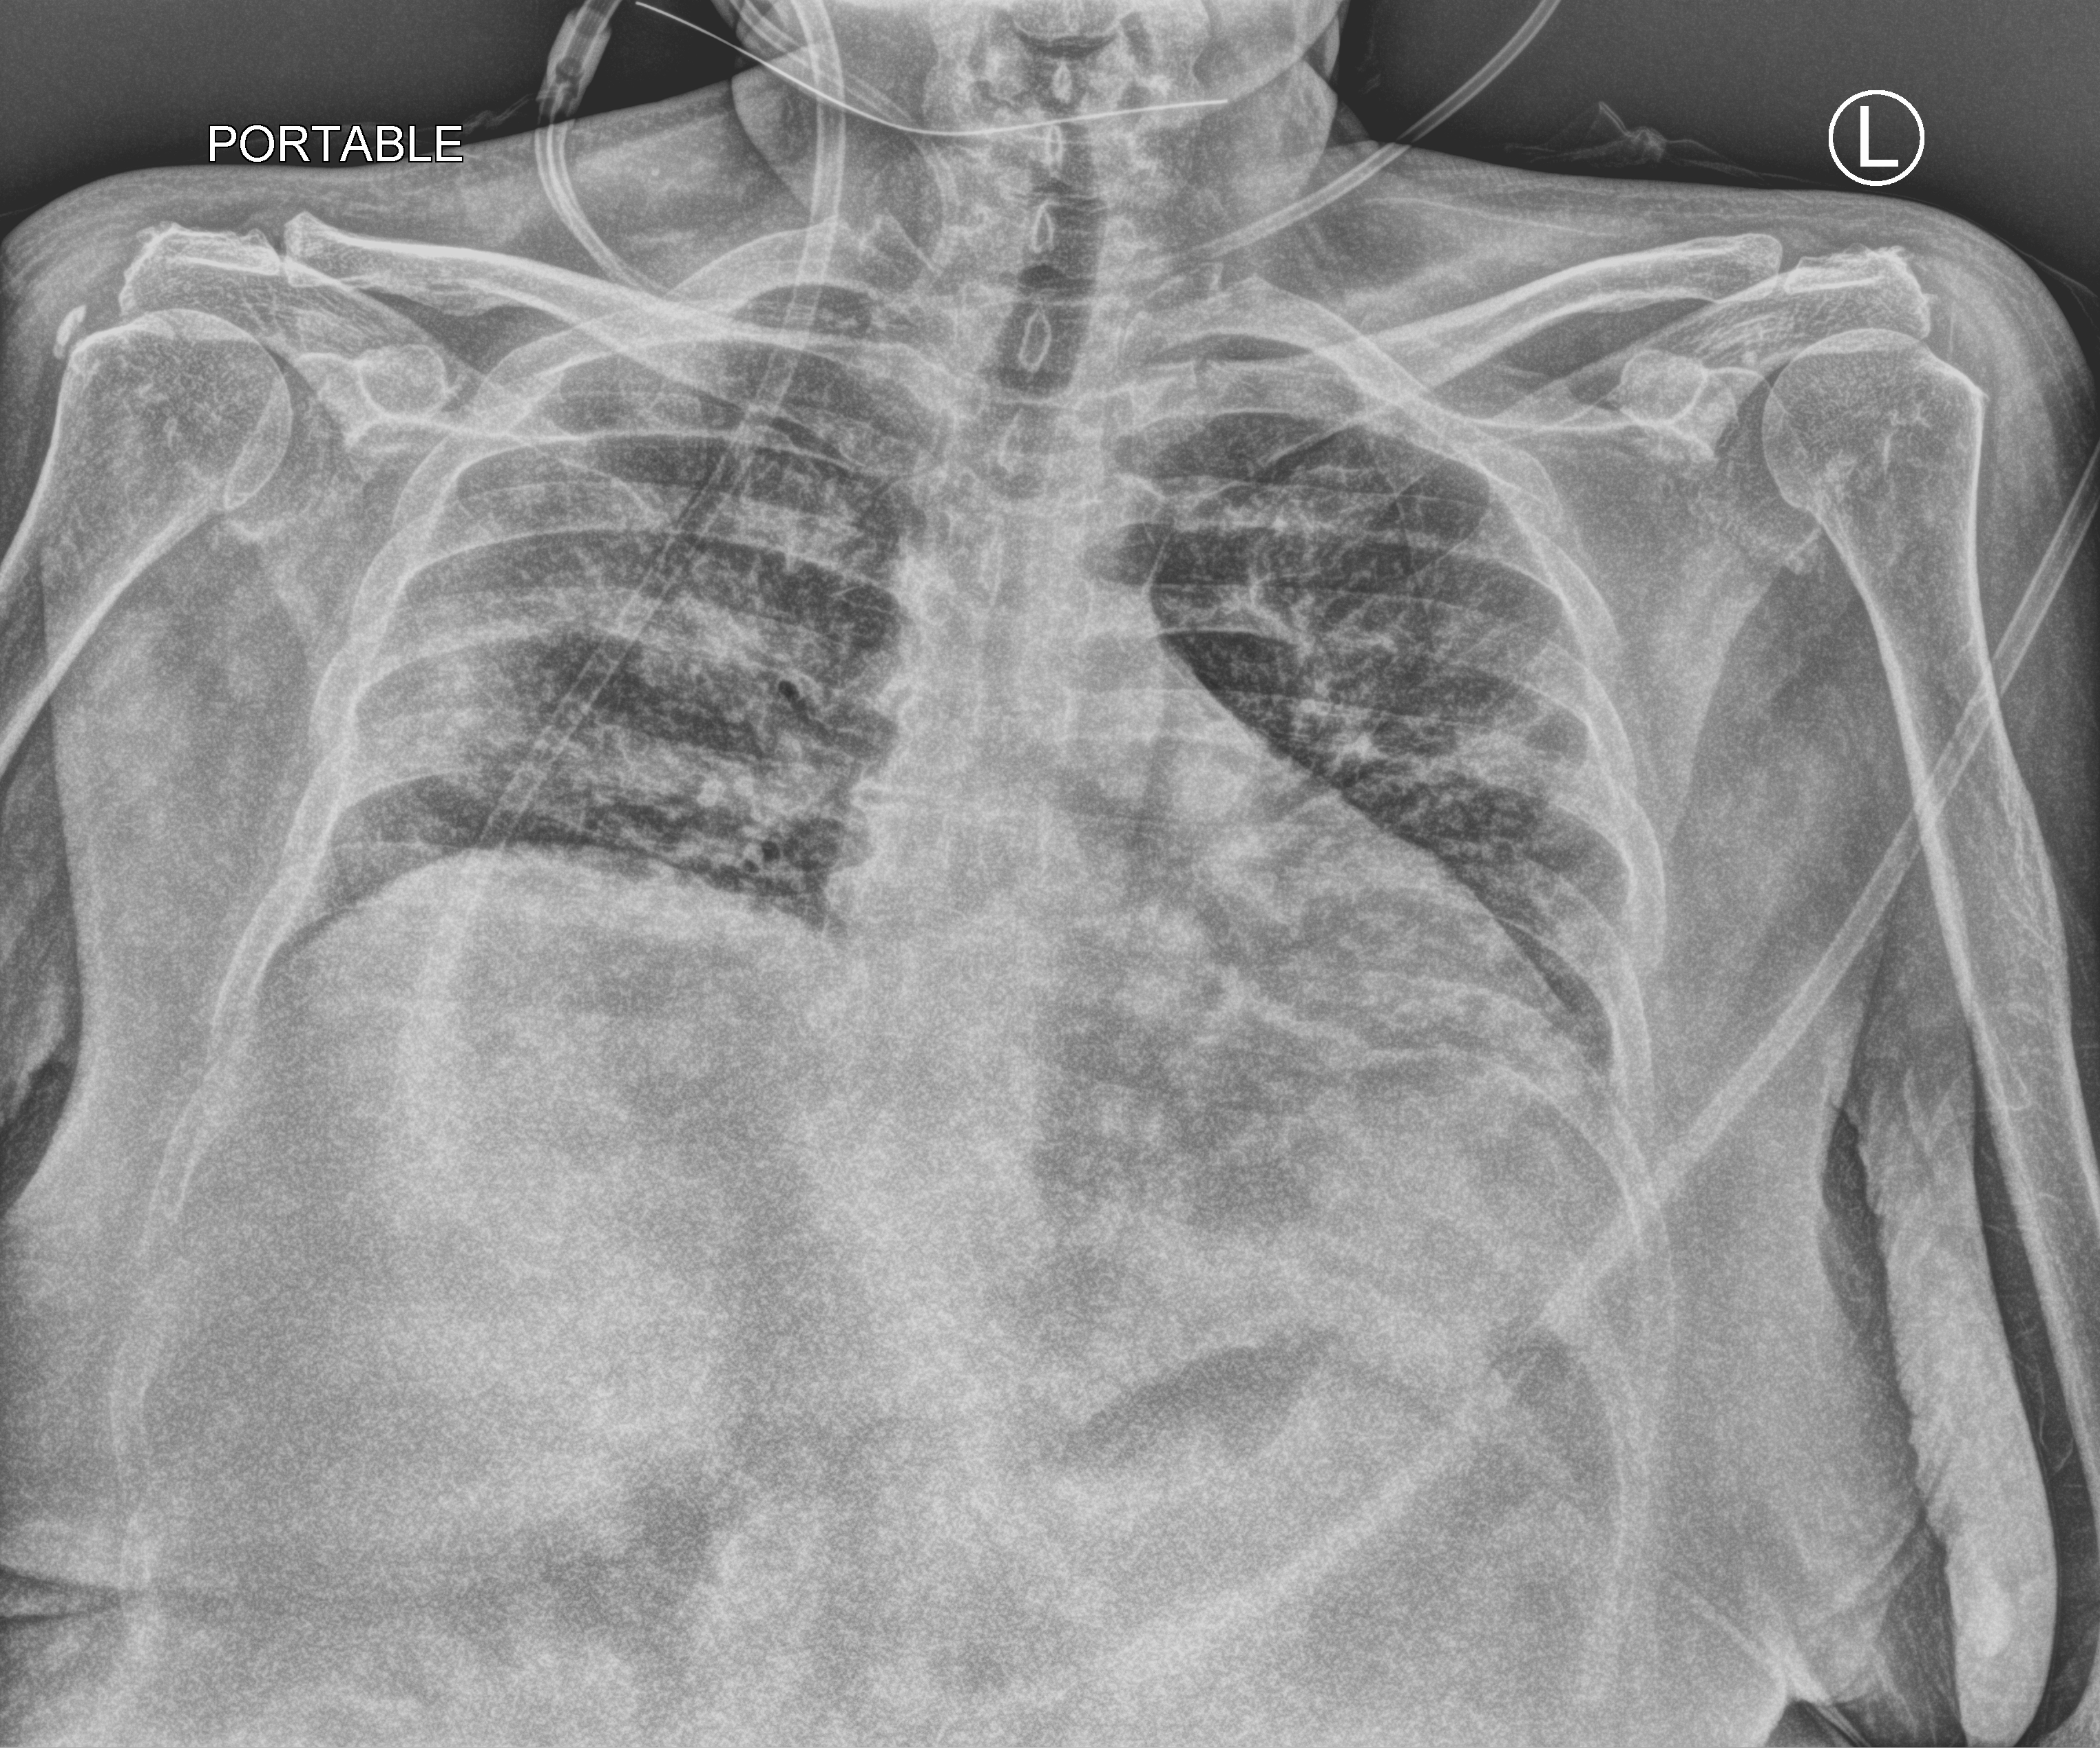
Bedside chest radiograph (computed radiography). Patient hospitalised with COVID-19; female, aged 18–59 years.
From the hospital-stay record, not from the radiograph (when in the stay this image was taken is not recorded): smoking status (admission record): never; mechanically ventilated during this hospital stay: no; admitted to intensive care during this hospital stay: yes.